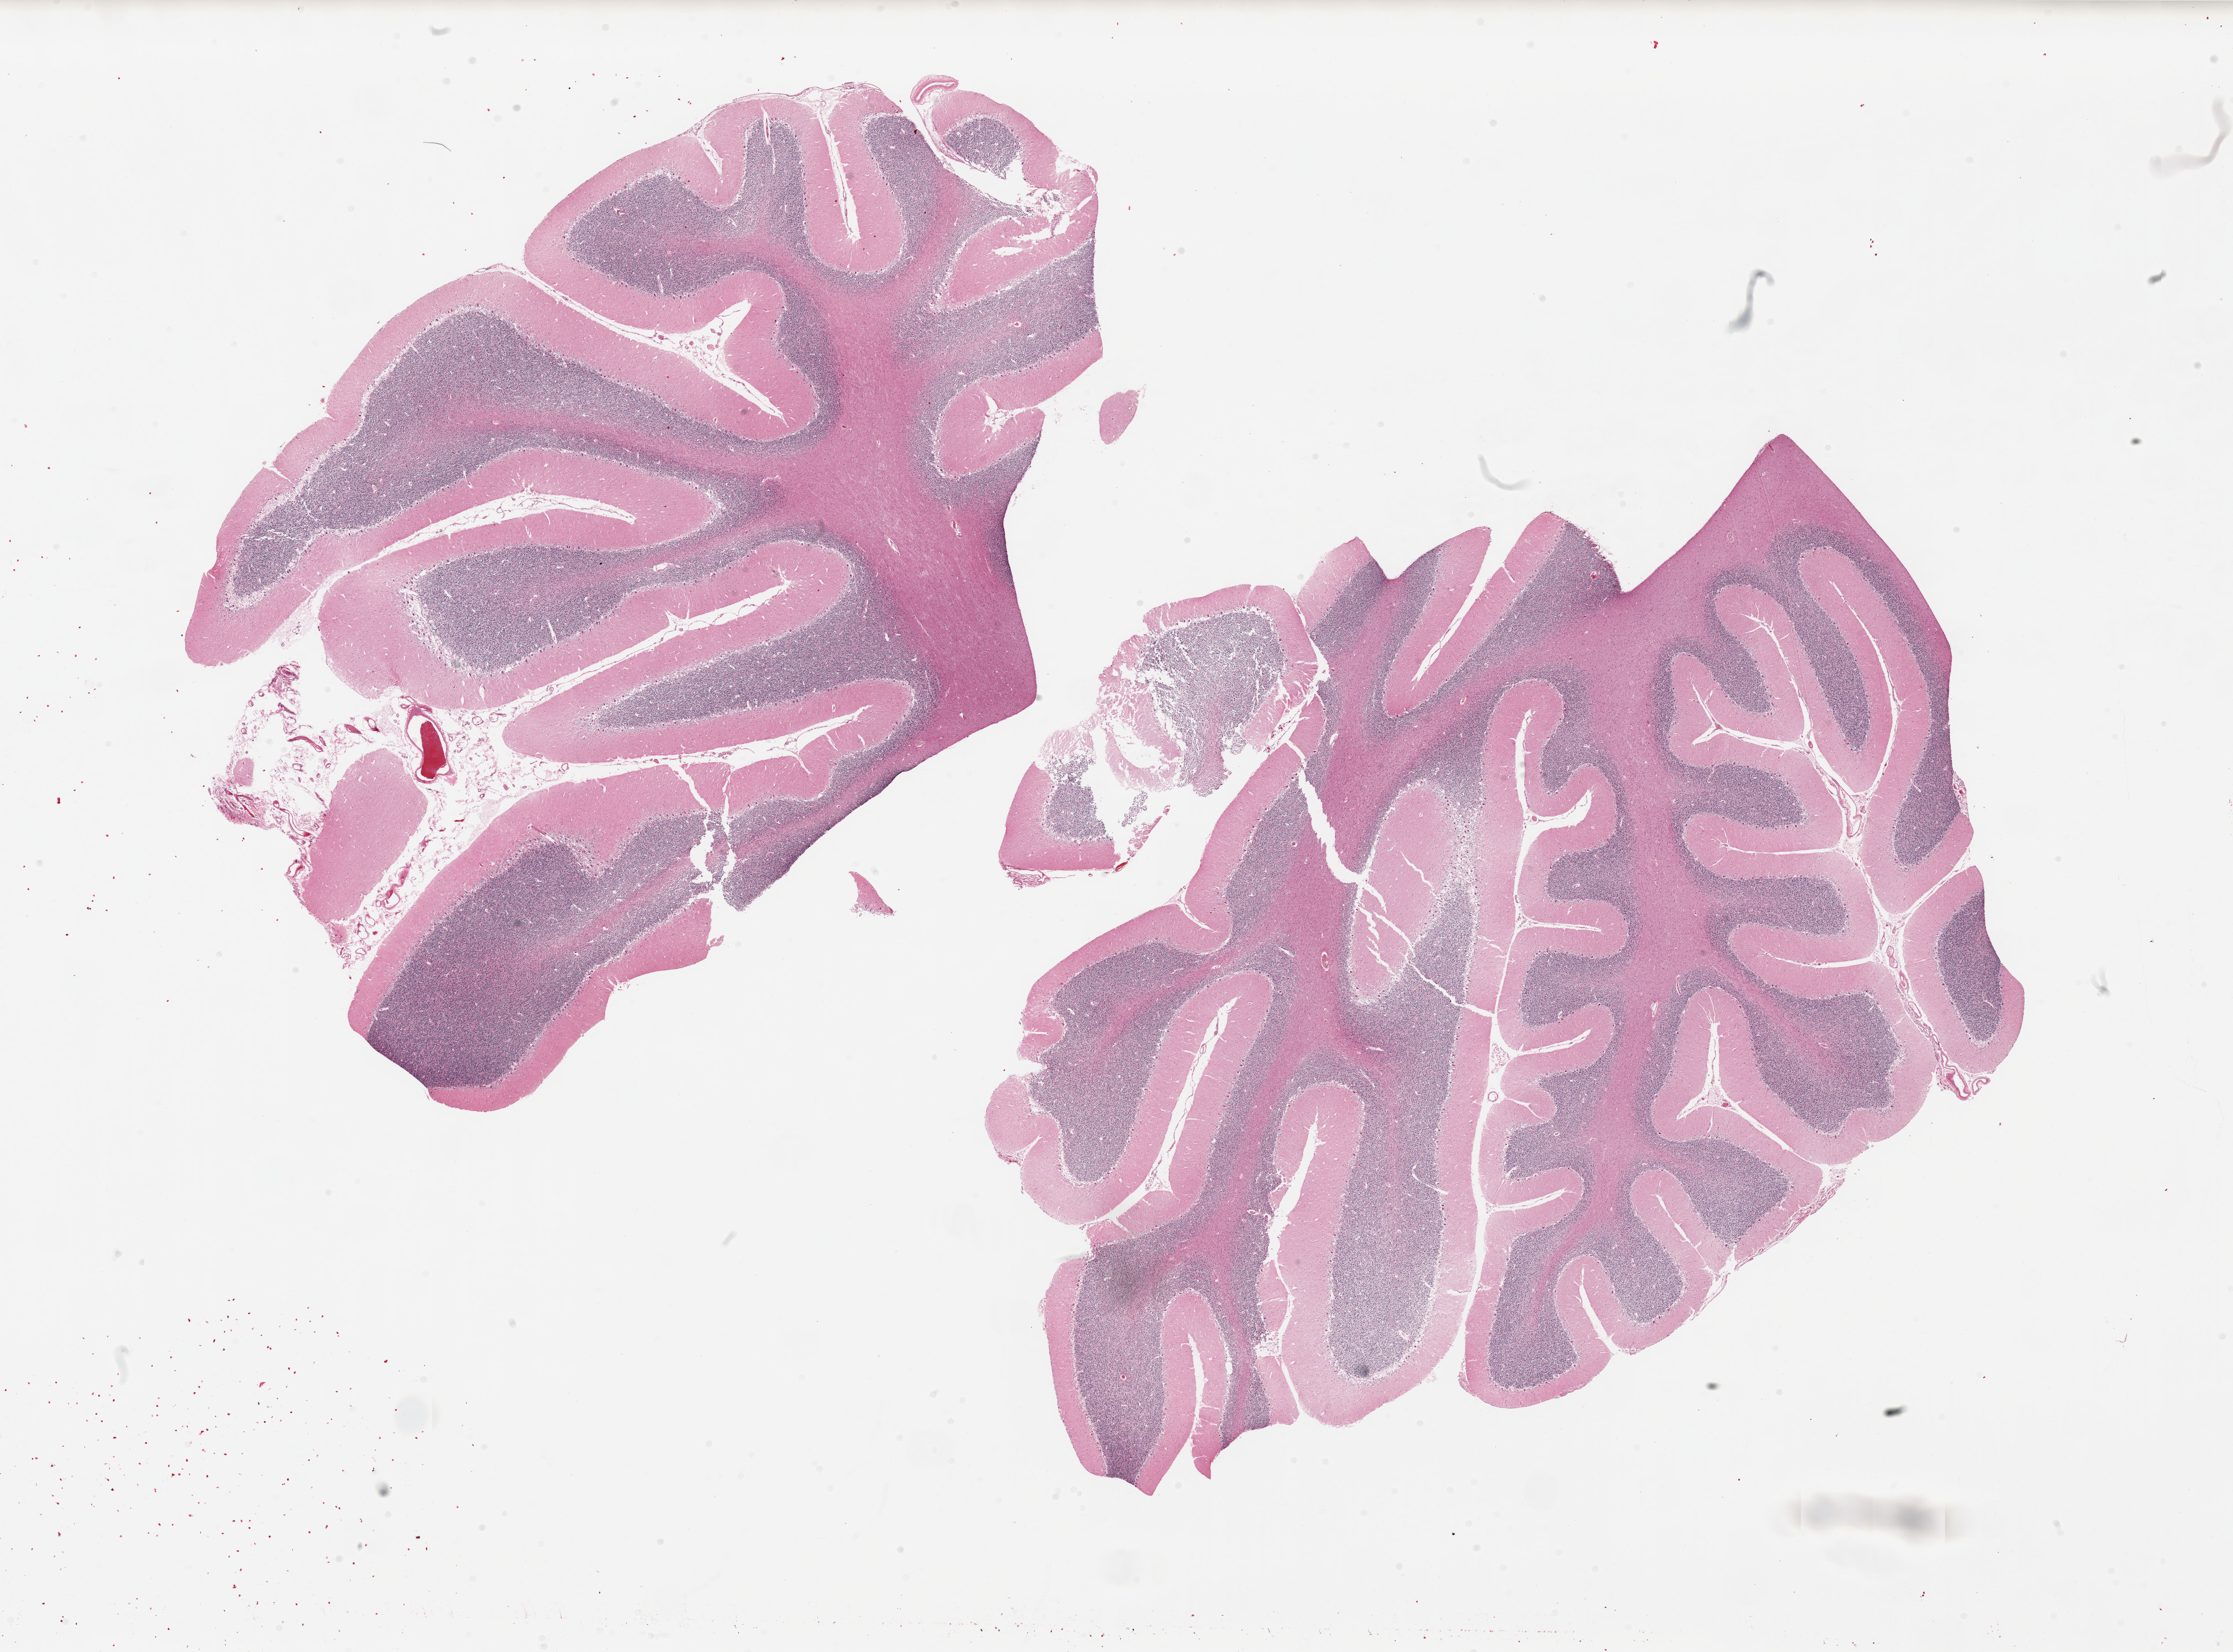
Digitized hematoxylin and eosin (H&E)-stained section, brightfield, a low-resolution overview of the entire scanned area, about 30.5 x 22.6 mm, PAXgene-fixed, paraffin-embedded tissue, section of cerebellum (target tissue), tissue donor sample. Donor sex: male.
Reviewer comment on this tissue sample: 2 pieces, unusually edematous.